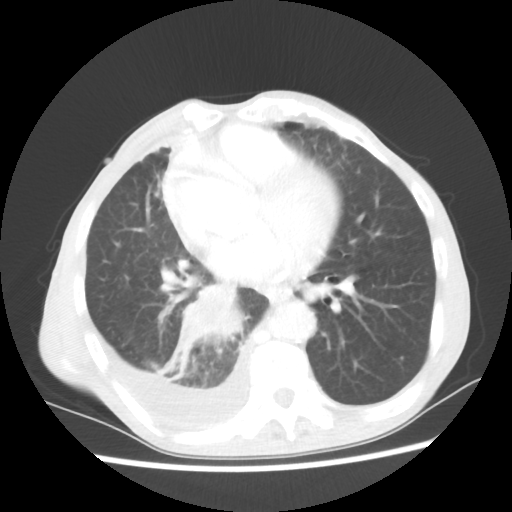
Chest CT, one axial slice. Position 26 of 60 along the scan axis. Reconstruction kernel STANDARD. Lung window (W 1500 / L -600 HU). 512 × 512 image matrix. Patient: male, 76 years. Case-level facts recorded for this patient, not image findings: clinical TNM (as recorded): T3 N3 M1a.
Structures marked on this image (rectangle marked by the reading radiologist):
- lung tumour (recorded histology: squamous cell carcinoma): box from (x=161, y=282) to (x=255, y=383) px